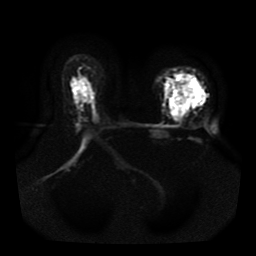
Breast MRI, one axial slice; slice 28 of 41 in the series (ordered by position); diffusion-weighted series; image 2 of 4 stored at this slice position (different b-values; order by instance number); 1.5 T; 256 × 256 image matrix, field of view 330 × 330 mm. Female patient.
Structures marked on this image (manually delineated by an expert):
- tumour on diffusion-weighted imaging: bounding box <166,74,205,121> (left, top, right, bottom; pixels)